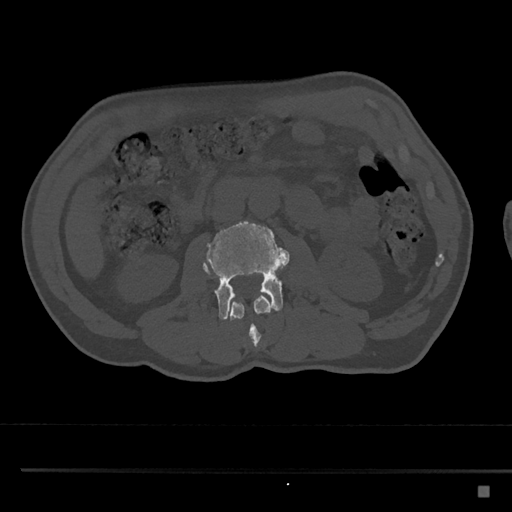
CT including the spine, one axial slice. Position 720 of 797 along the scan axis. Reconstruction kernel Br40s/3. 120 kVp. Bone window (W 1800 / L 400 HU). 0.5 mm slice thickness. 512 × 512 image matrix. Patient: male, 59 years. Case-level facts recorded for this patient, not image findings: primary cancer: prostate.
Outlined on this slice (semi-automatically segmented with operator editing):
- L2 vertebra: bounding box <205,268,273,346> (left, top, right, bottom; pixels)
- L3 vertebra: <202,221,290,320>